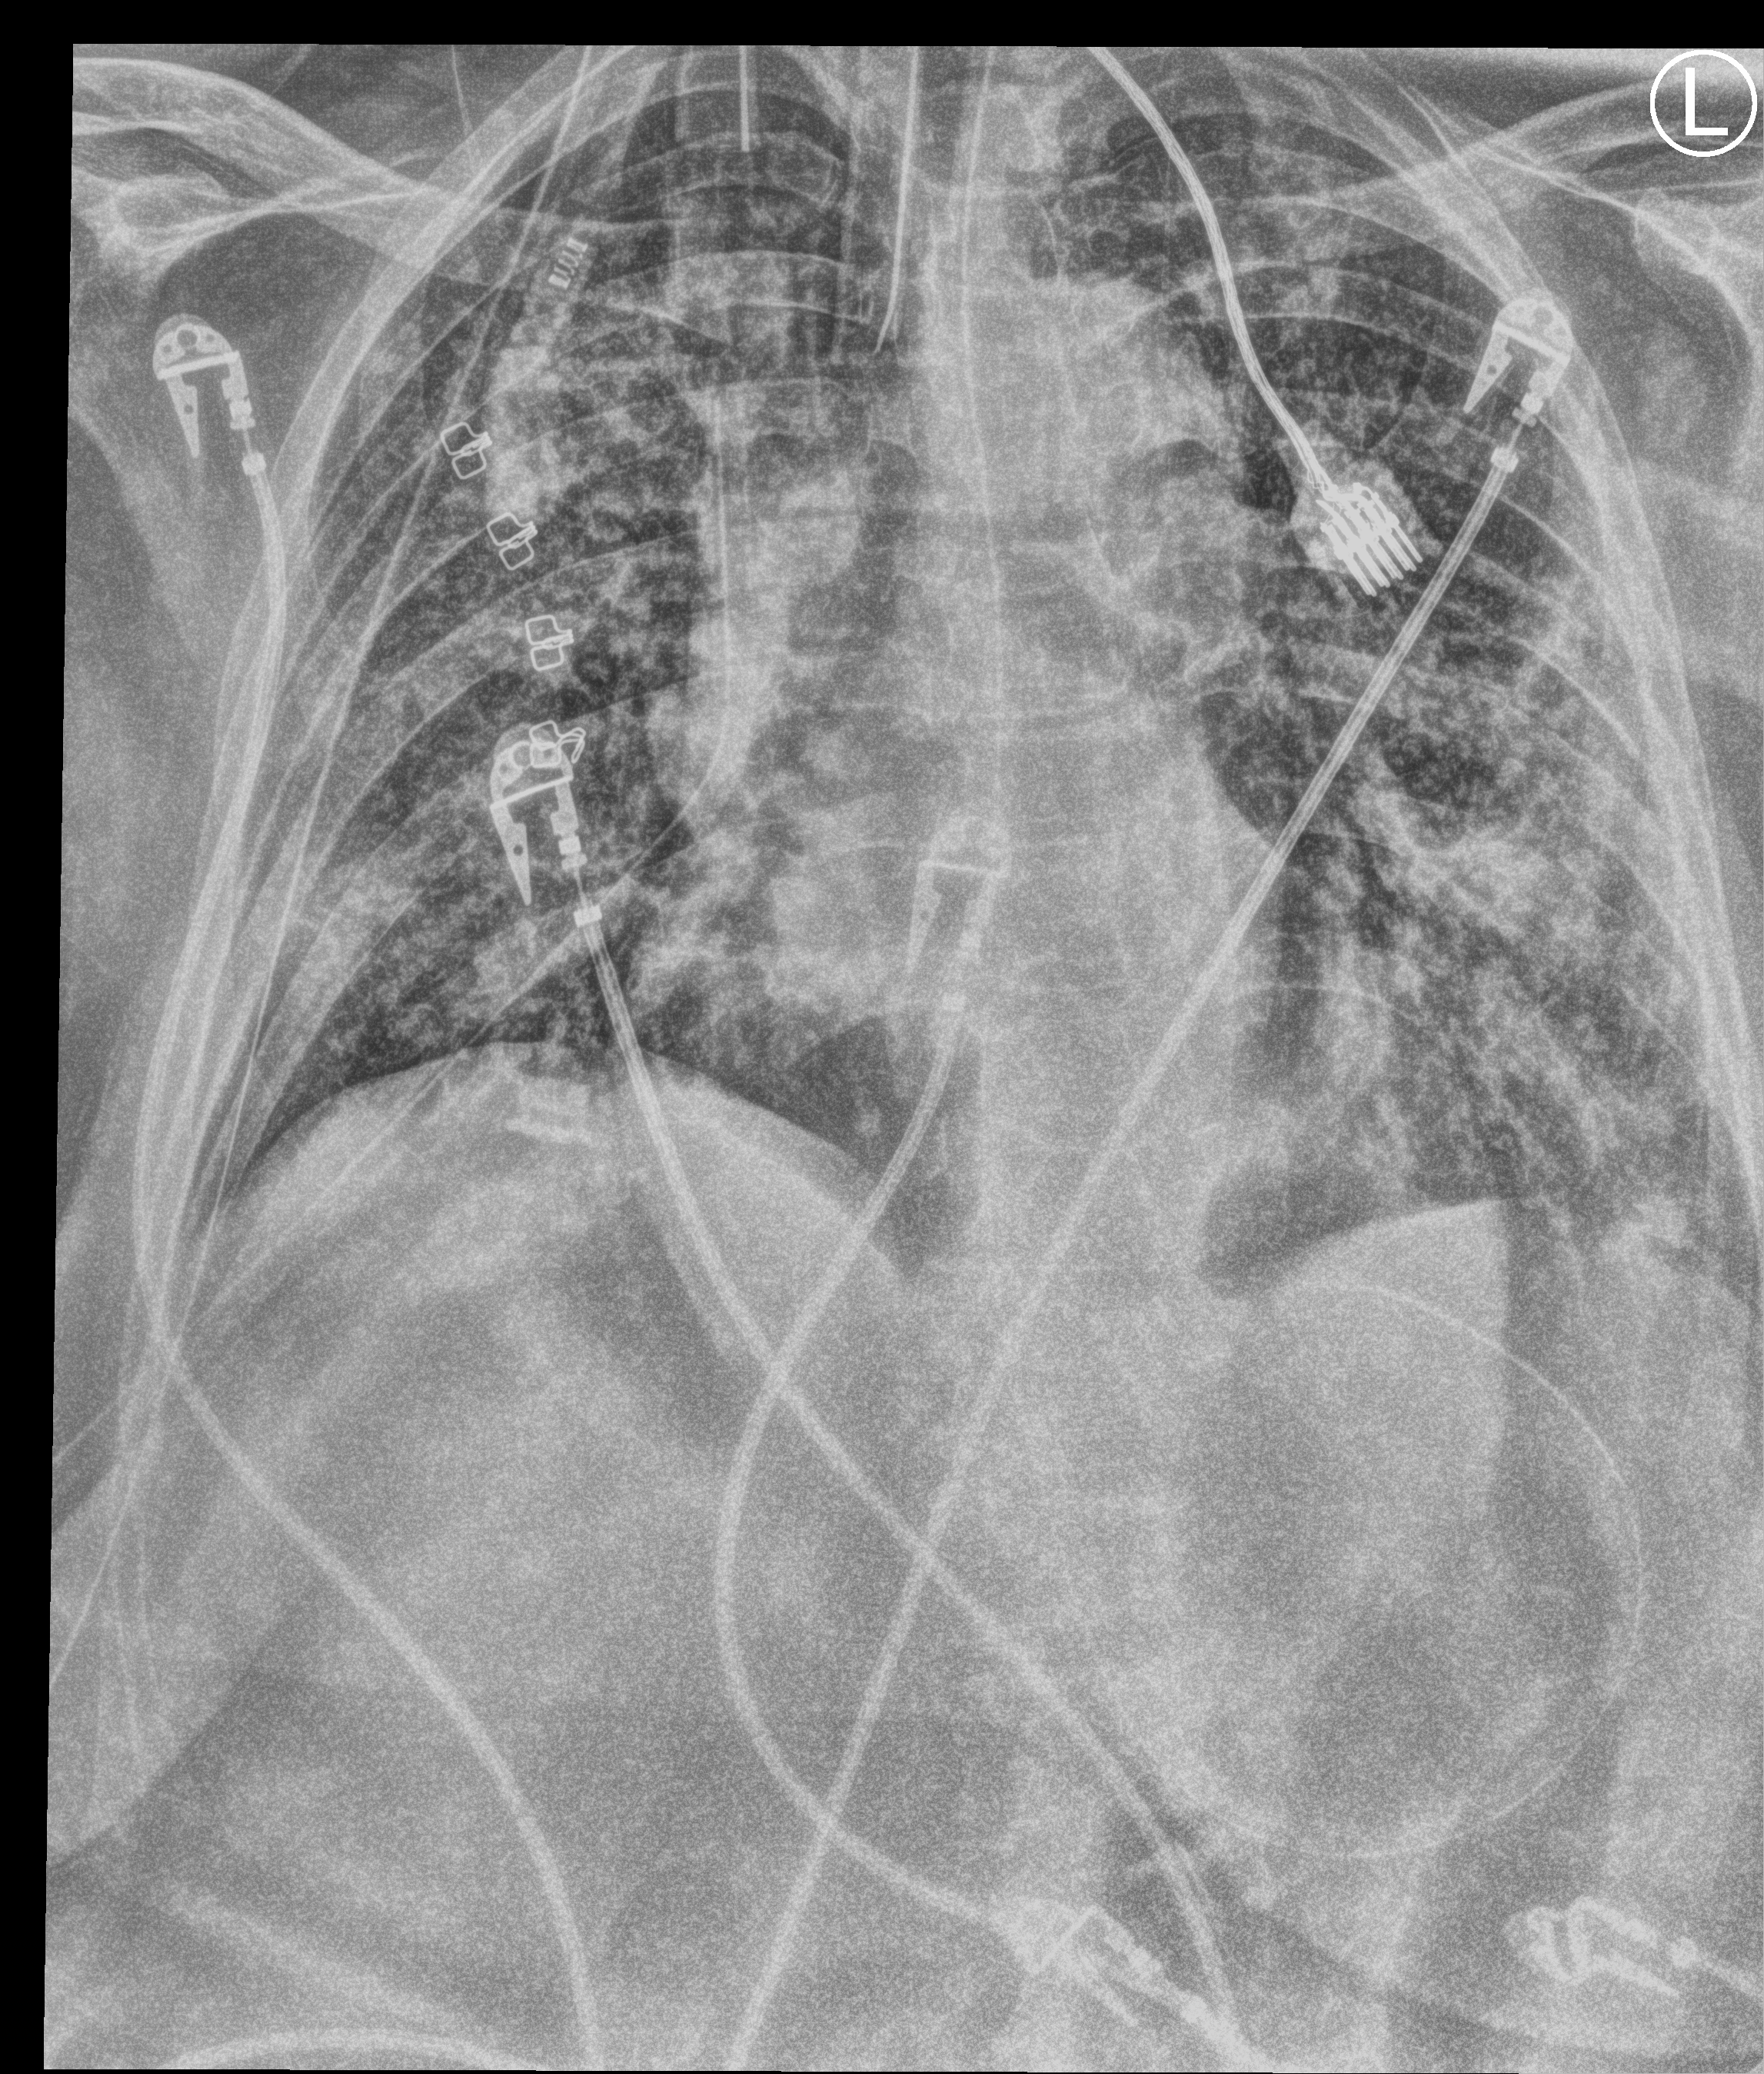
Bedside chest radiograph (computed radiography). Female patient hospitalised with COVID-19, age 60–74 years.
Hospital-stay facts (about this admission, not read from this image; timing relative to this image not recorded):
- admitted to intensive care during this hospital stay: yes